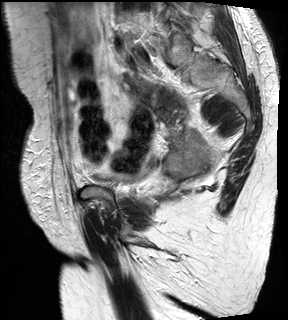
Pelvic MRI for cervical cancer, one sagittal slice. Position 9 of 28 along the scan axis. T2-weighted. 1.5 T. TE 89 ms, TR 2740 ms. 4 mm slice thickness. 288 × 320 image matrix, field of view 234 × 260 mm. Patient: female, 59 years.
Annotated regions visible in this slice (manually delineated by an expert):
- uterus and cervix: bounding box (x1, y1, x2, y2) in pixels: (146, 84, 215, 184)